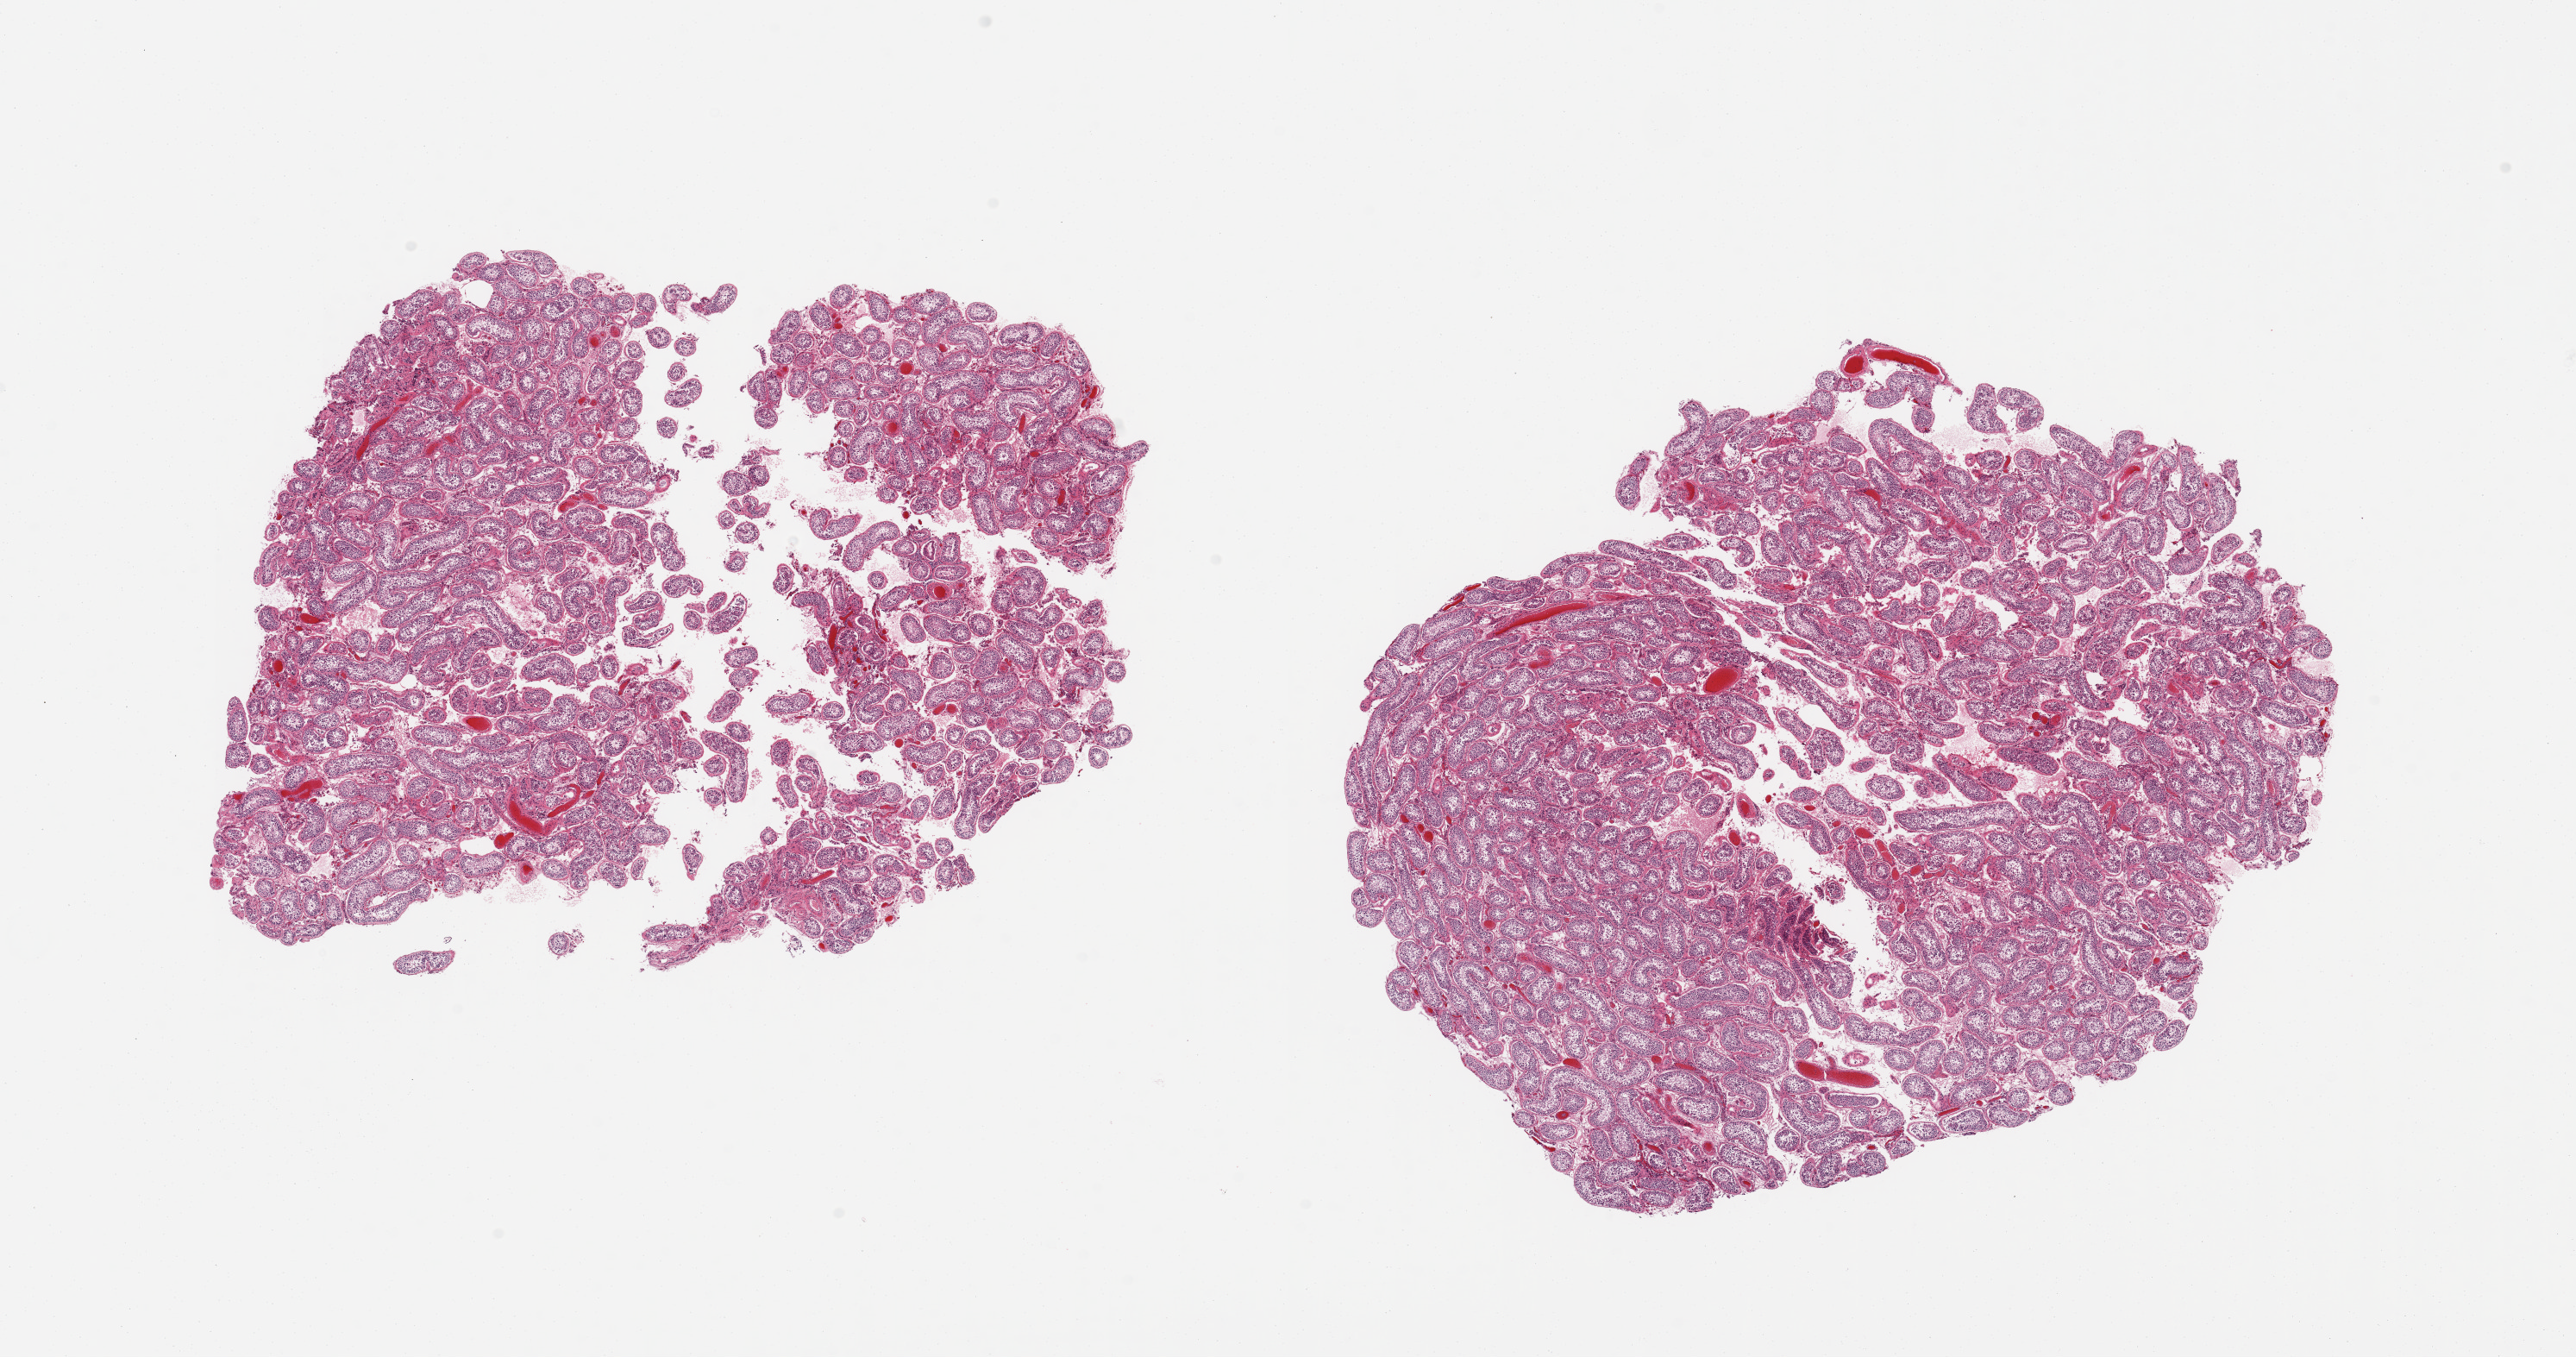
Whole-slide image, H&E stain — a low-resolution overview of the entire scanned area, about 23.6 x 12.4 mm (from a 20x scan), PAXgene-fixed paraffin-embedded (PFPE) section, sampled site (target tissue): testis, donor tissue sample. Donor sex: male.
Reviewer comment on this tissue sample: 2 pieces; active spermatogenesis.